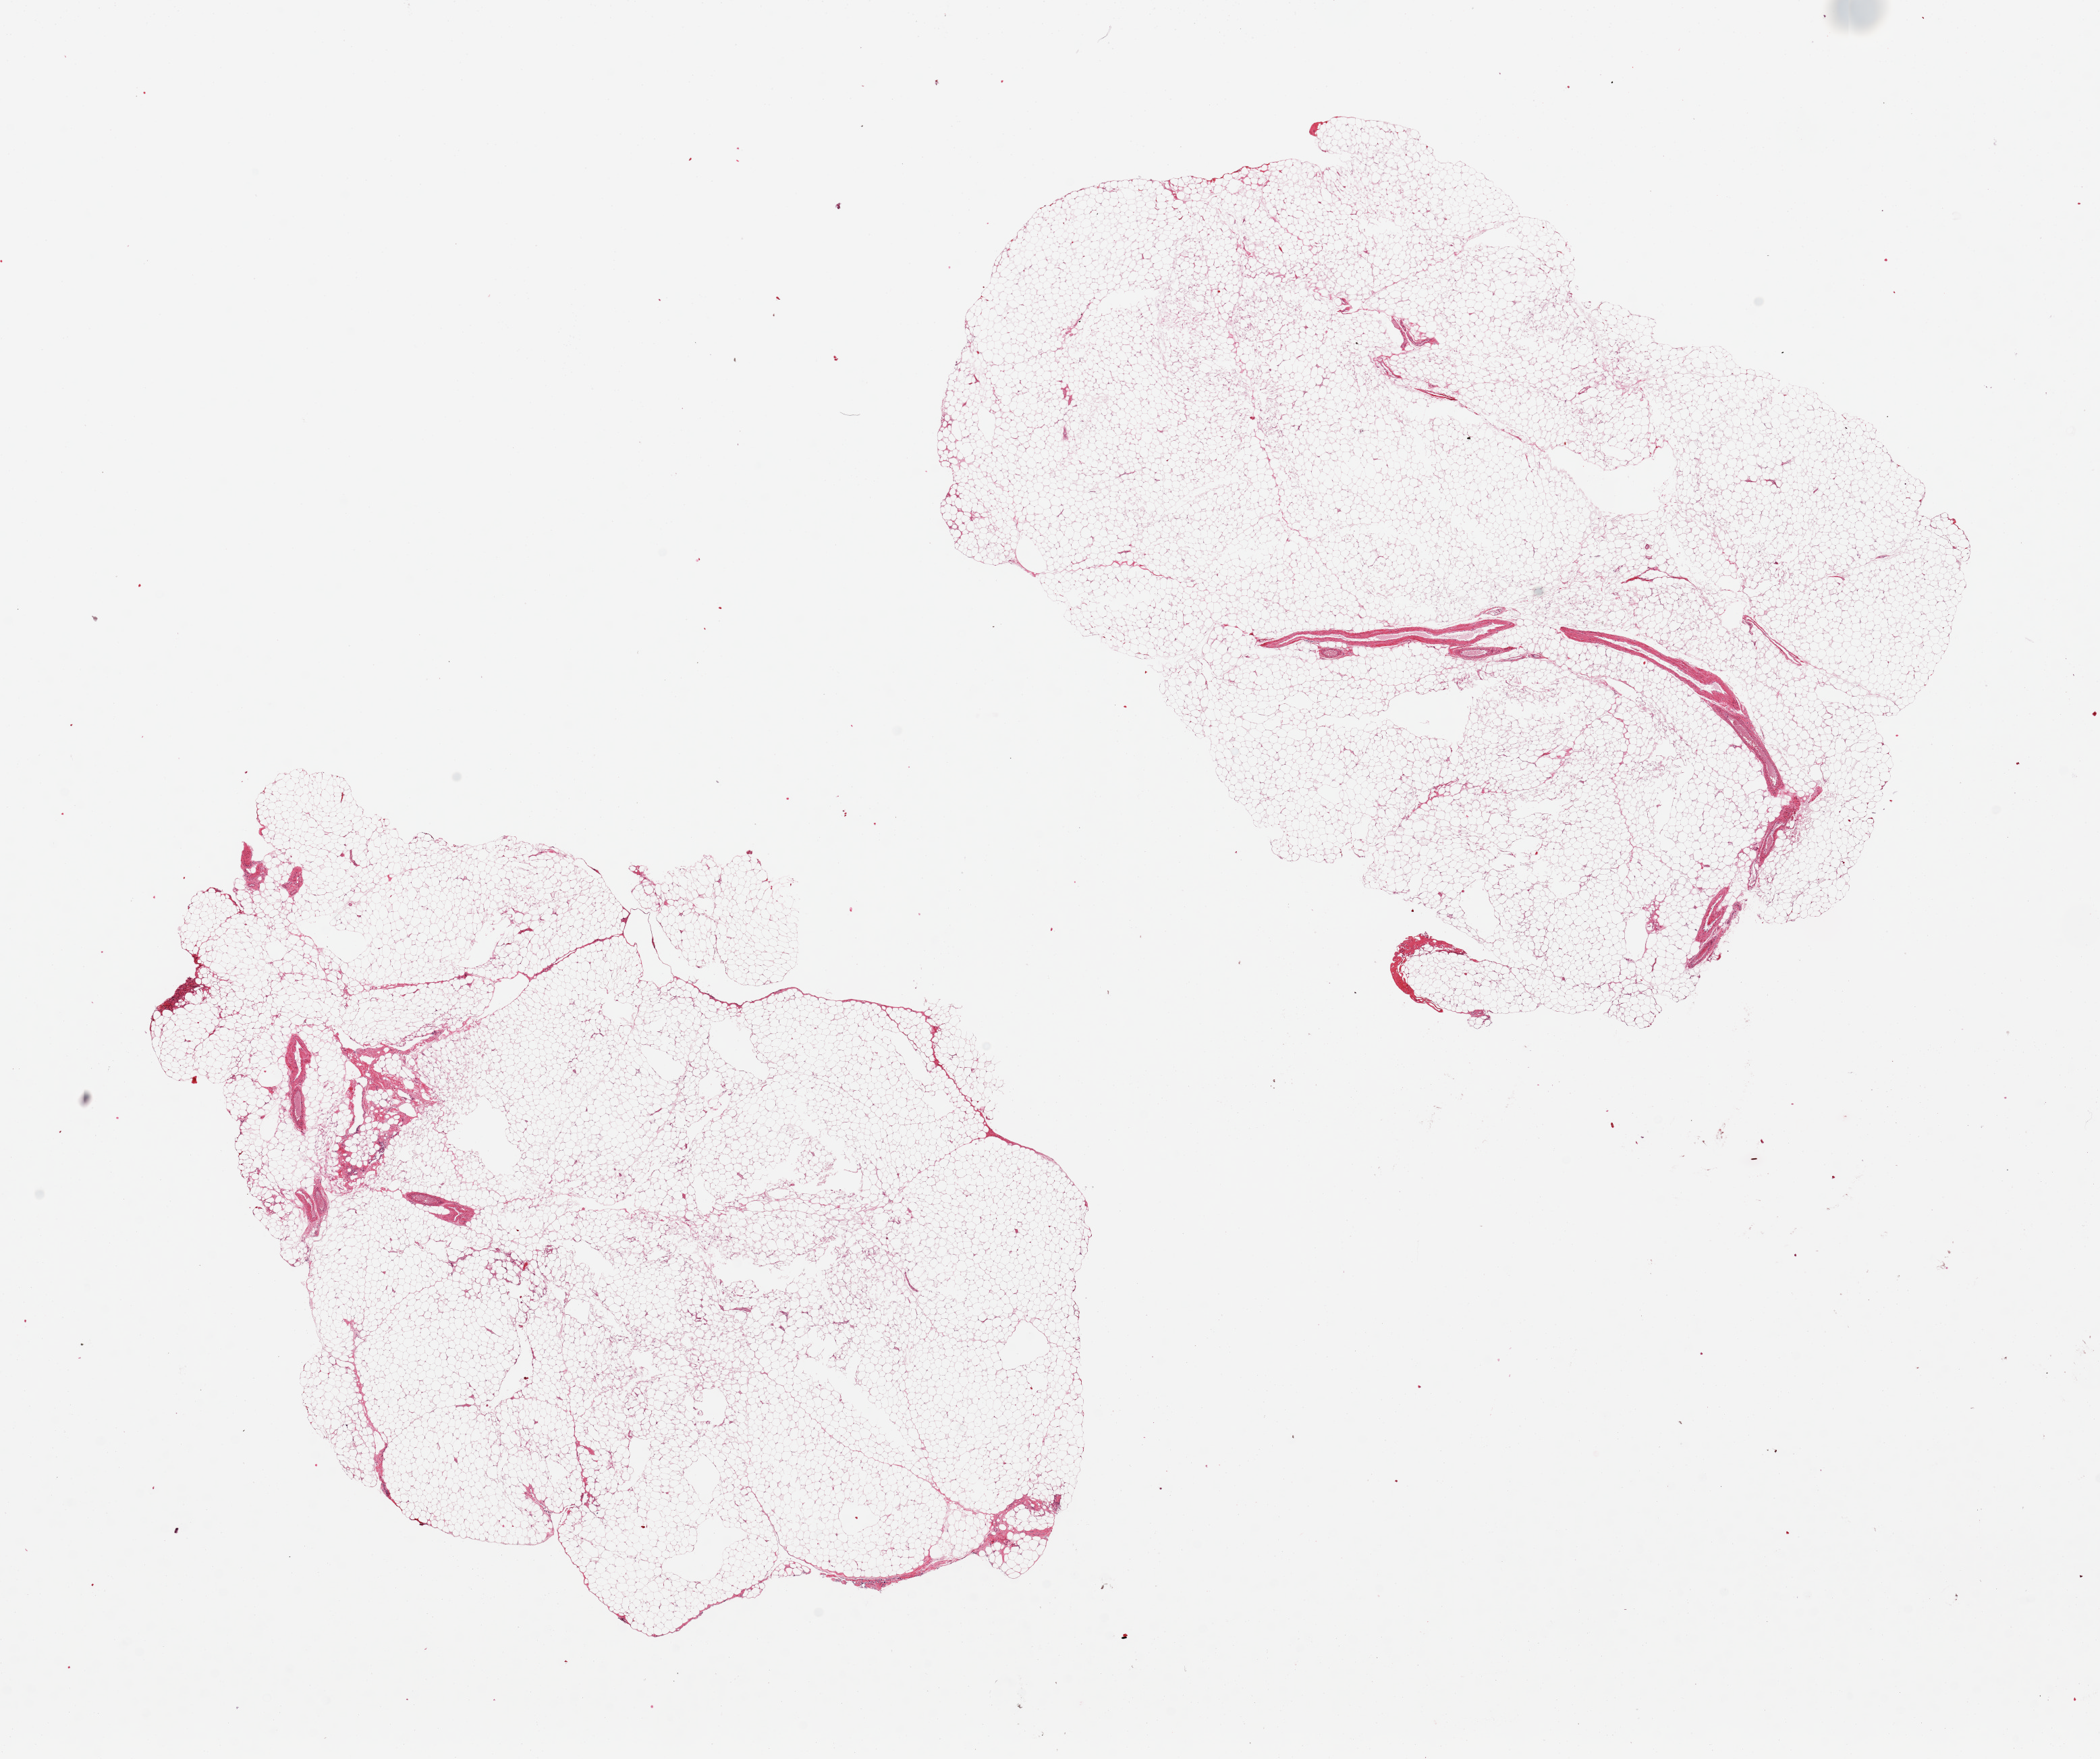
Hematoxylin and eosin (H&E) whole-slide image, shown as a low-resolution overview of the whole scanned area (about 24.6 x 20.6 mm, acquisition: 20x scan), PAXgene-fixed paraffin-embedded (PFPE) section, target tissue: omentum, tissue donor sample. Donor: male.
Reviewer comment on this tissue sample: 2 pieces.